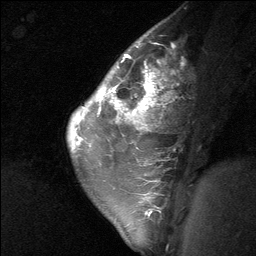
Breast MRI (dynamic contrast-enhanced), one sagittal slice; position 47 of 64 along the scan axis; dynamic contrast-enhanced study with each time point stored as its own series, time point 2 of 3 at this slice position (early post-contrast, ordered by acquisition time); 1.5 T; TE 4.8 ms, TR 27 ms; 2 mm slice thickness; 256 × 256 image matrix, field of view 180 × 180 mm. Female patient, age 26 years. From the clinical record (not read from this slice): setting: breast cancer imaged before/during neoadjuvant chemotherapy; receptor status: HR-positive, HER2-negative.
Annotated regions visible in this slice (semi-automatically segmented with operator editing):
- analysis volume of interest (the breast-tissue region the enhancement analysis was run in; not a lesion): bounding box [x1, y1, x2, y2] px = [86, 43, 176, 138]
- tumour enhancement mask (voxels above the 90 % enhancement threshold inside the analysis volume of interest): [100, 55, 166, 113]